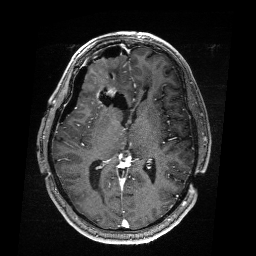
Brain MRI from a brain-tumour surgery series, one axial slice; T1-weighted post-contrast; 1 mm slice thickness; 256 × 256 image matrix, field of view 256 × 256 mm. Case-level facts recorded for this patient, not image findings: histopathology: Astrocytoma; WHO grade: 4; IDH mutation: yes; tumour location: Right Frontal.
Structures marked on this image (manually delineated by an expert):
- residual tumour: bounding box (x1, y1, x2, y2) in pixels: (90, 82, 119, 93)